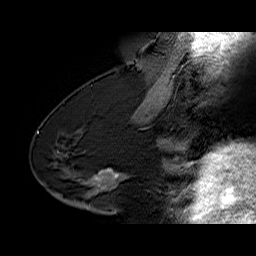
Breast MRI (dynamic contrast-enhanced), one sagittal slice; position 32 of 60 along the scan axis; dynamic contrast-enhanced series, time point 2 of 6 at this slice position (early post-contrast); 1.5 T; TE 6.4 ms, TR 32.9 ms; 4 mm slice thickness; 256 × 256 image matrix, field of view 200 × 200 mm. Female patient. Case-level facts recorded for this patient, not image findings: setting: breast cancer imaged before/during neoadjuvant chemotherapy; receptor status: HR-positive, HER2-negative.
Outlined on this slice (semi-automatically segmented with operator editing):
- analysis volume of interest (the breast-tissue region the enhancement analysis was run in; not a lesion): bounding box (x1, y1, x2, y2) in pixels: (68, 169, 129, 203)
- tumour enhancement mask (voxels above the 100 % enhancement threshold inside the analysis volume of interest): (91, 169, 125, 185)